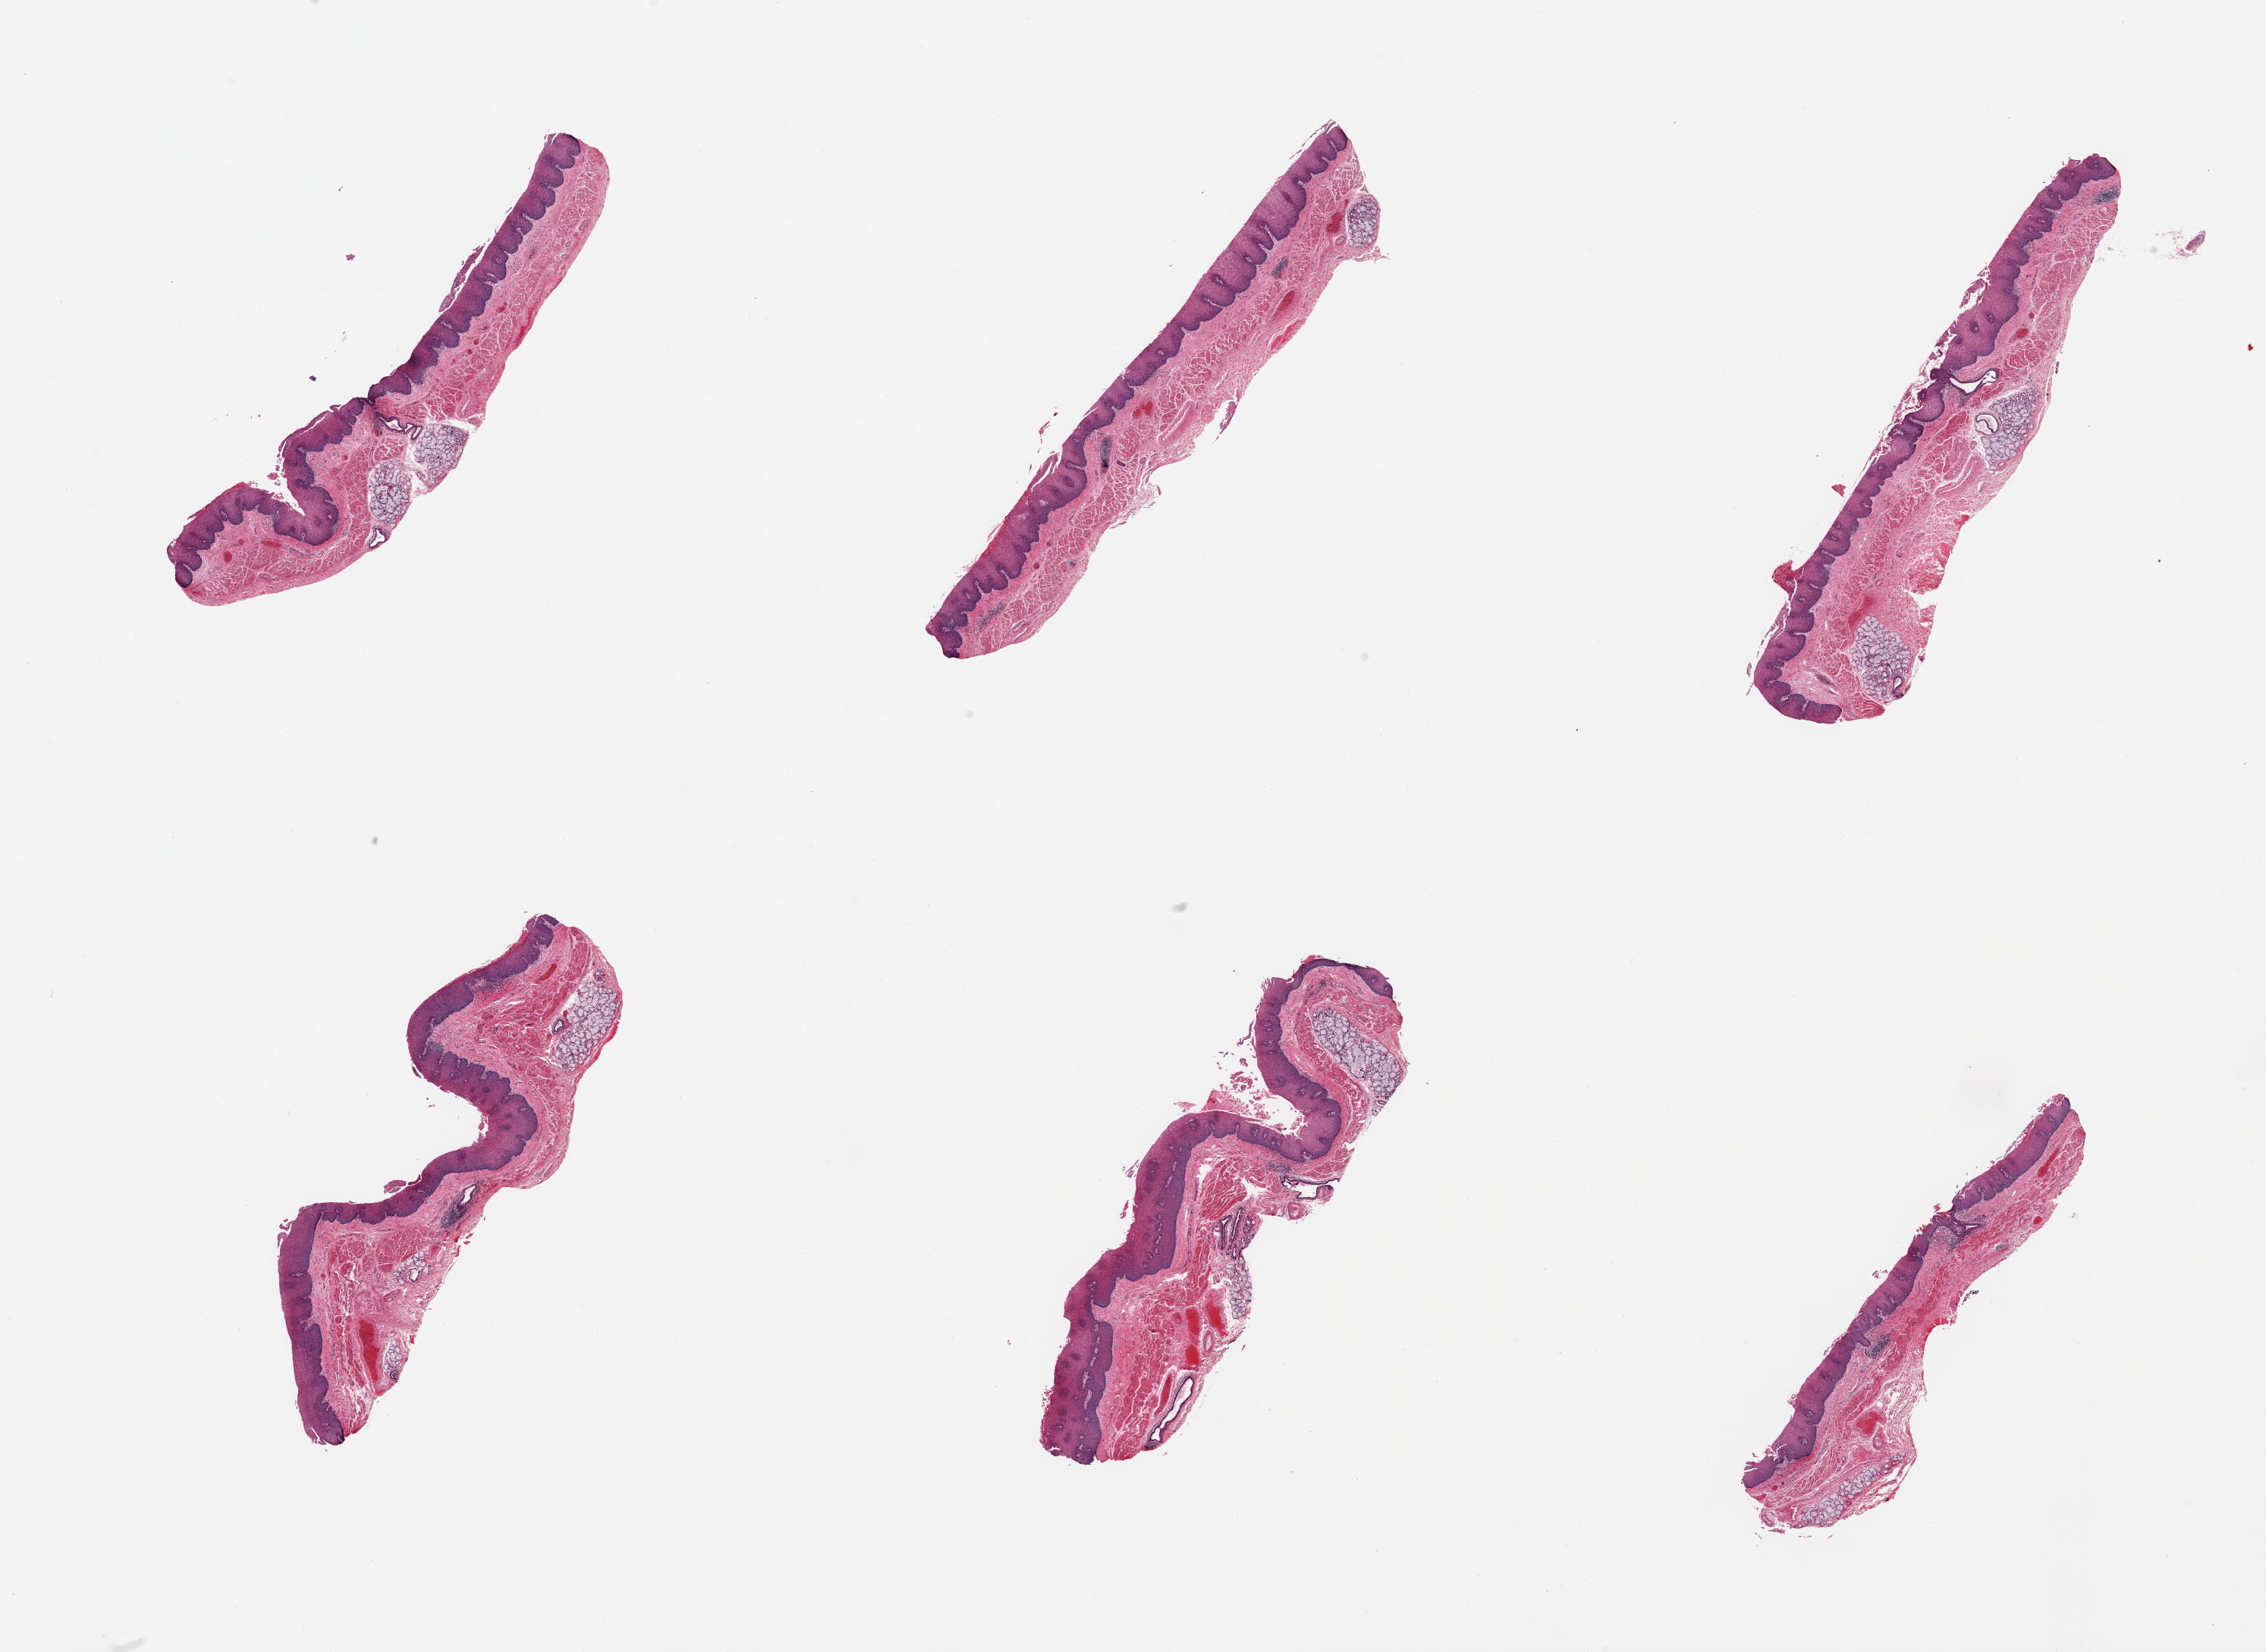
H&E whole-slide image — shown as a low-resolution overview of the whole scanned area (about 23.6 x 17.2 mm, from a 20x scan). PAXgene-fixed paraffin-embedded (PFPE) section. Sampled site (target tissue): esophageal mucous membrane. Donor tissue sample. Donor: male.
• review note (as recorded): 6 pieces, squamous mucosa is ~0.4mm, ~30-40% thickness